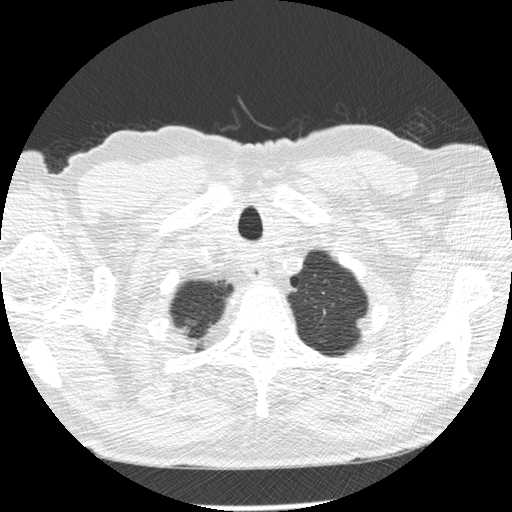
Low-dose screening chest CT, axial slice. Second annual screen. Lung window (W 1500 / L -600 HU). 2.5 mm slice thickness. Standard (soft-tissue) reconstruction kernel (STANDARD). Male, age 73 years at enrolment. Former smoker at enrolment.
• Lesion marked by an expert reader, bounding box <344,306,384,345> (left, top, right, bottom; pixels).
• No non-calcified nodule or mass ≥4 mm was recorded by the screening reader at this exam.
• Official screen result: negative screen, minor abnormalities not suspicious for lung cancer.
• Lung cancer was diagnosed 457 days after this screen (after the third annual screen): adenocarcinoma, NOS, left upper lobe, poorly differentiated (G3), stage IB (AJCC 6th edition), 10 mm at pathology.